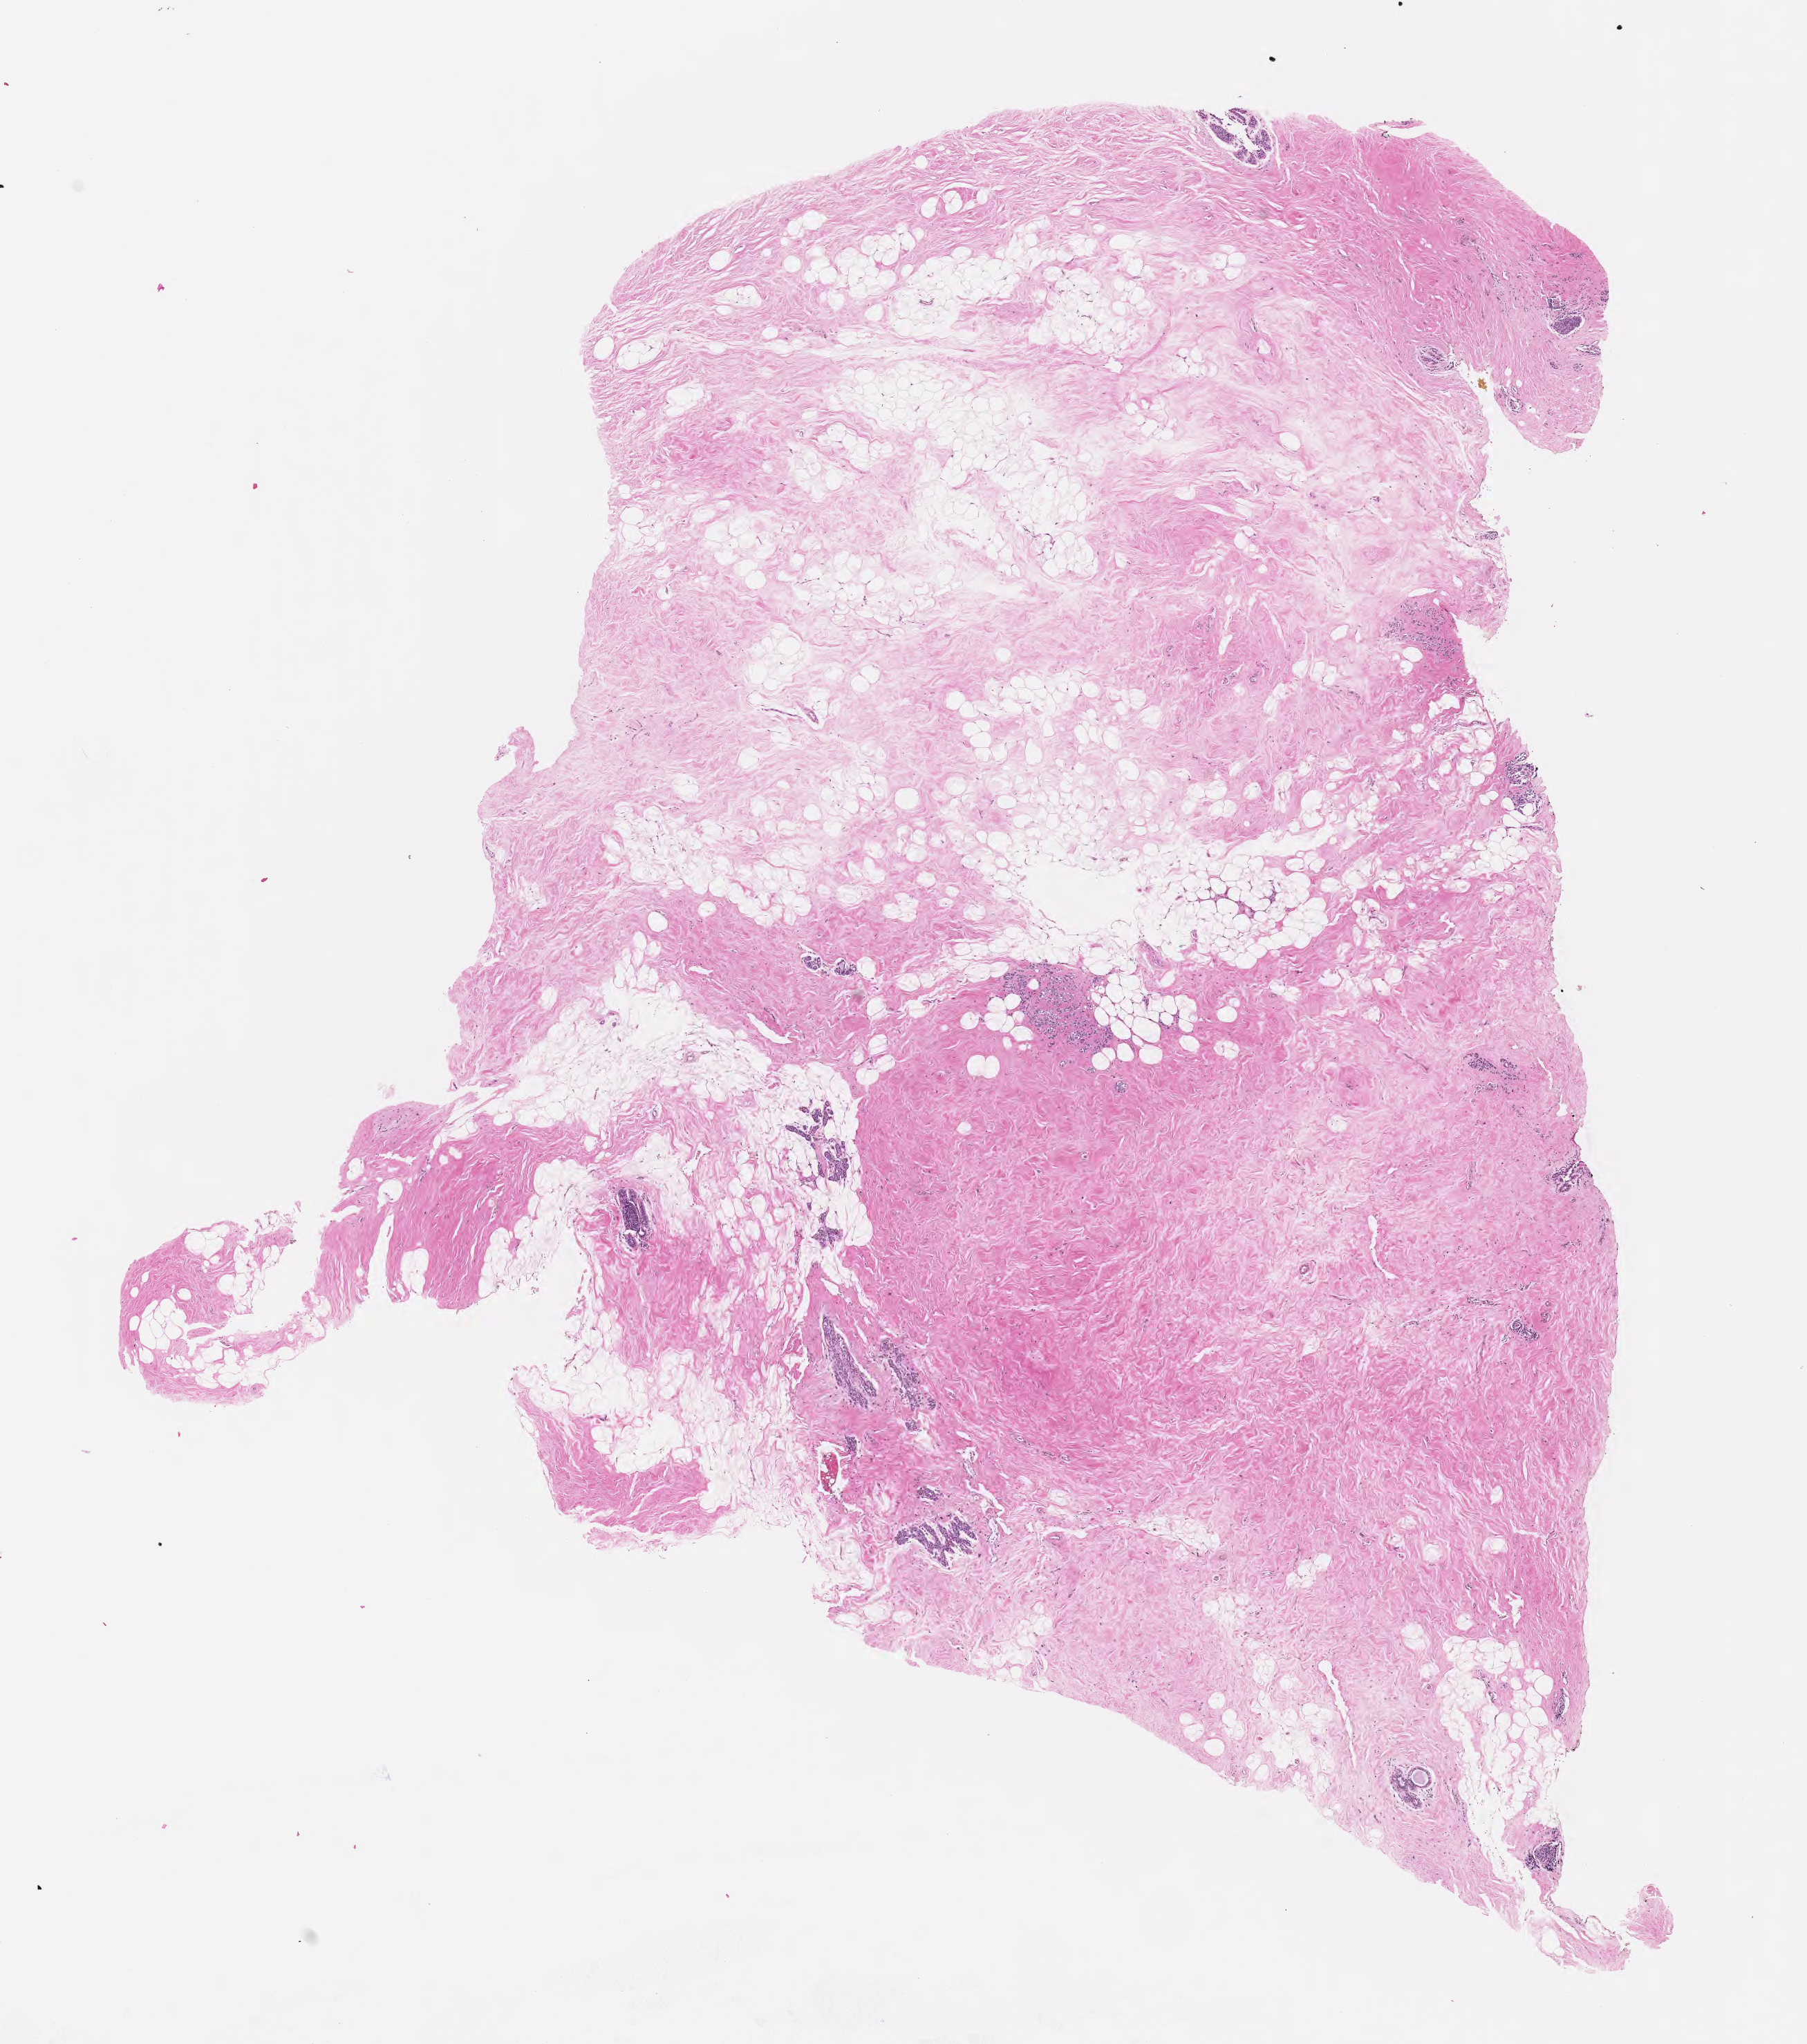
H&E whole-slide image — shown as a low-resolution overview of the whole scanned area (about 10.6 x 12.0 mm), formalin-fixed, paraffin-embedded (FFPE) tissue, primary tumor, anatomic site: breast. Female patient; age at initial diagnosis 57 years. Tumor grade: G2 (moderately differentiated). Composition of this section per pathologist review: tumor cells 35%, tumor nuclei 35%, stromal cells 15%, necrosis 0%, normal cells 50%. Infiltration values recorded for this section: lymphocyte infiltration 3%, monocyte infiltration 1%, neutrophil infiltration 6%.
- histologic diagnosis: Lobular carcinoma, NOS
- section: top of the tissue portion
- AJCC pathologic stage: Stage IIA